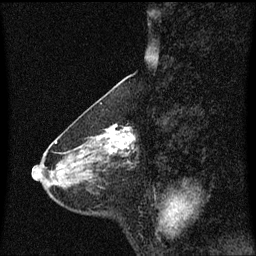
Breast MRI (dynamic contrast-enhanced), one sagittal slice; slice 24 of 60 in the series (ordered by position); dynamic contrast-enhanced series, image 2 of 3 at this slice position (ordered by acquisition); 1.5 T; TE 4.2 ms, TR 8.4 ms; 2 mm slice thickness; 256 × 256 image matrix. Female patient, age 58 years.
Structures marked on this image (semi-automatic segmentation, software-assisted and operator-edited):
- analysis volume of interest (the breast-tissue region the enhancement analysis was run in; not a lesion): box from (x=100, y=124) to (x=137, y=160) px
- tumour enhancement mask (voxels above the 70 % enhancement threshold inside the analysis volume of interest): (x=100, y=124)–(x=137, y=155)